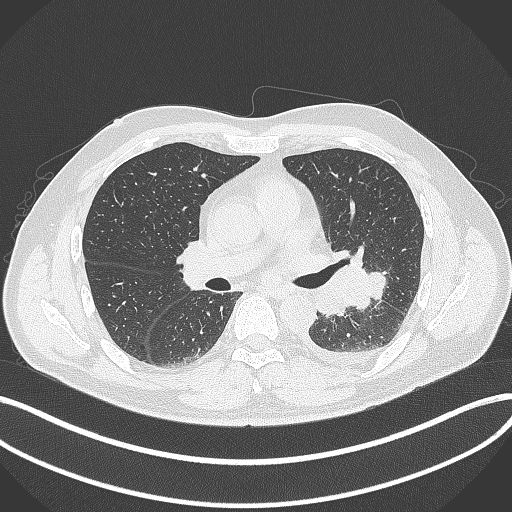
Chest CT, one axial slice. Slice 201 of 342 in the series (ordered by position). Reconstruction kernel B70f. 120 kVp. Lung window (W 1500 / L -600 HU). 1 mm slice thickness. 512 × 512 image matrix, field of view 400 × 400 mm. Male patient, age 58 years. From the clinical record (not read from this slice): clinical TNM (as recorded): T3 N1 M1b.
Structures marked on this image (bounding box drawn by a radiologist):
- lung tumour (recorded histology: small cell carcinoma): bounding box [x1, y1, x2, y2] px = [336, 257, 387, 312]